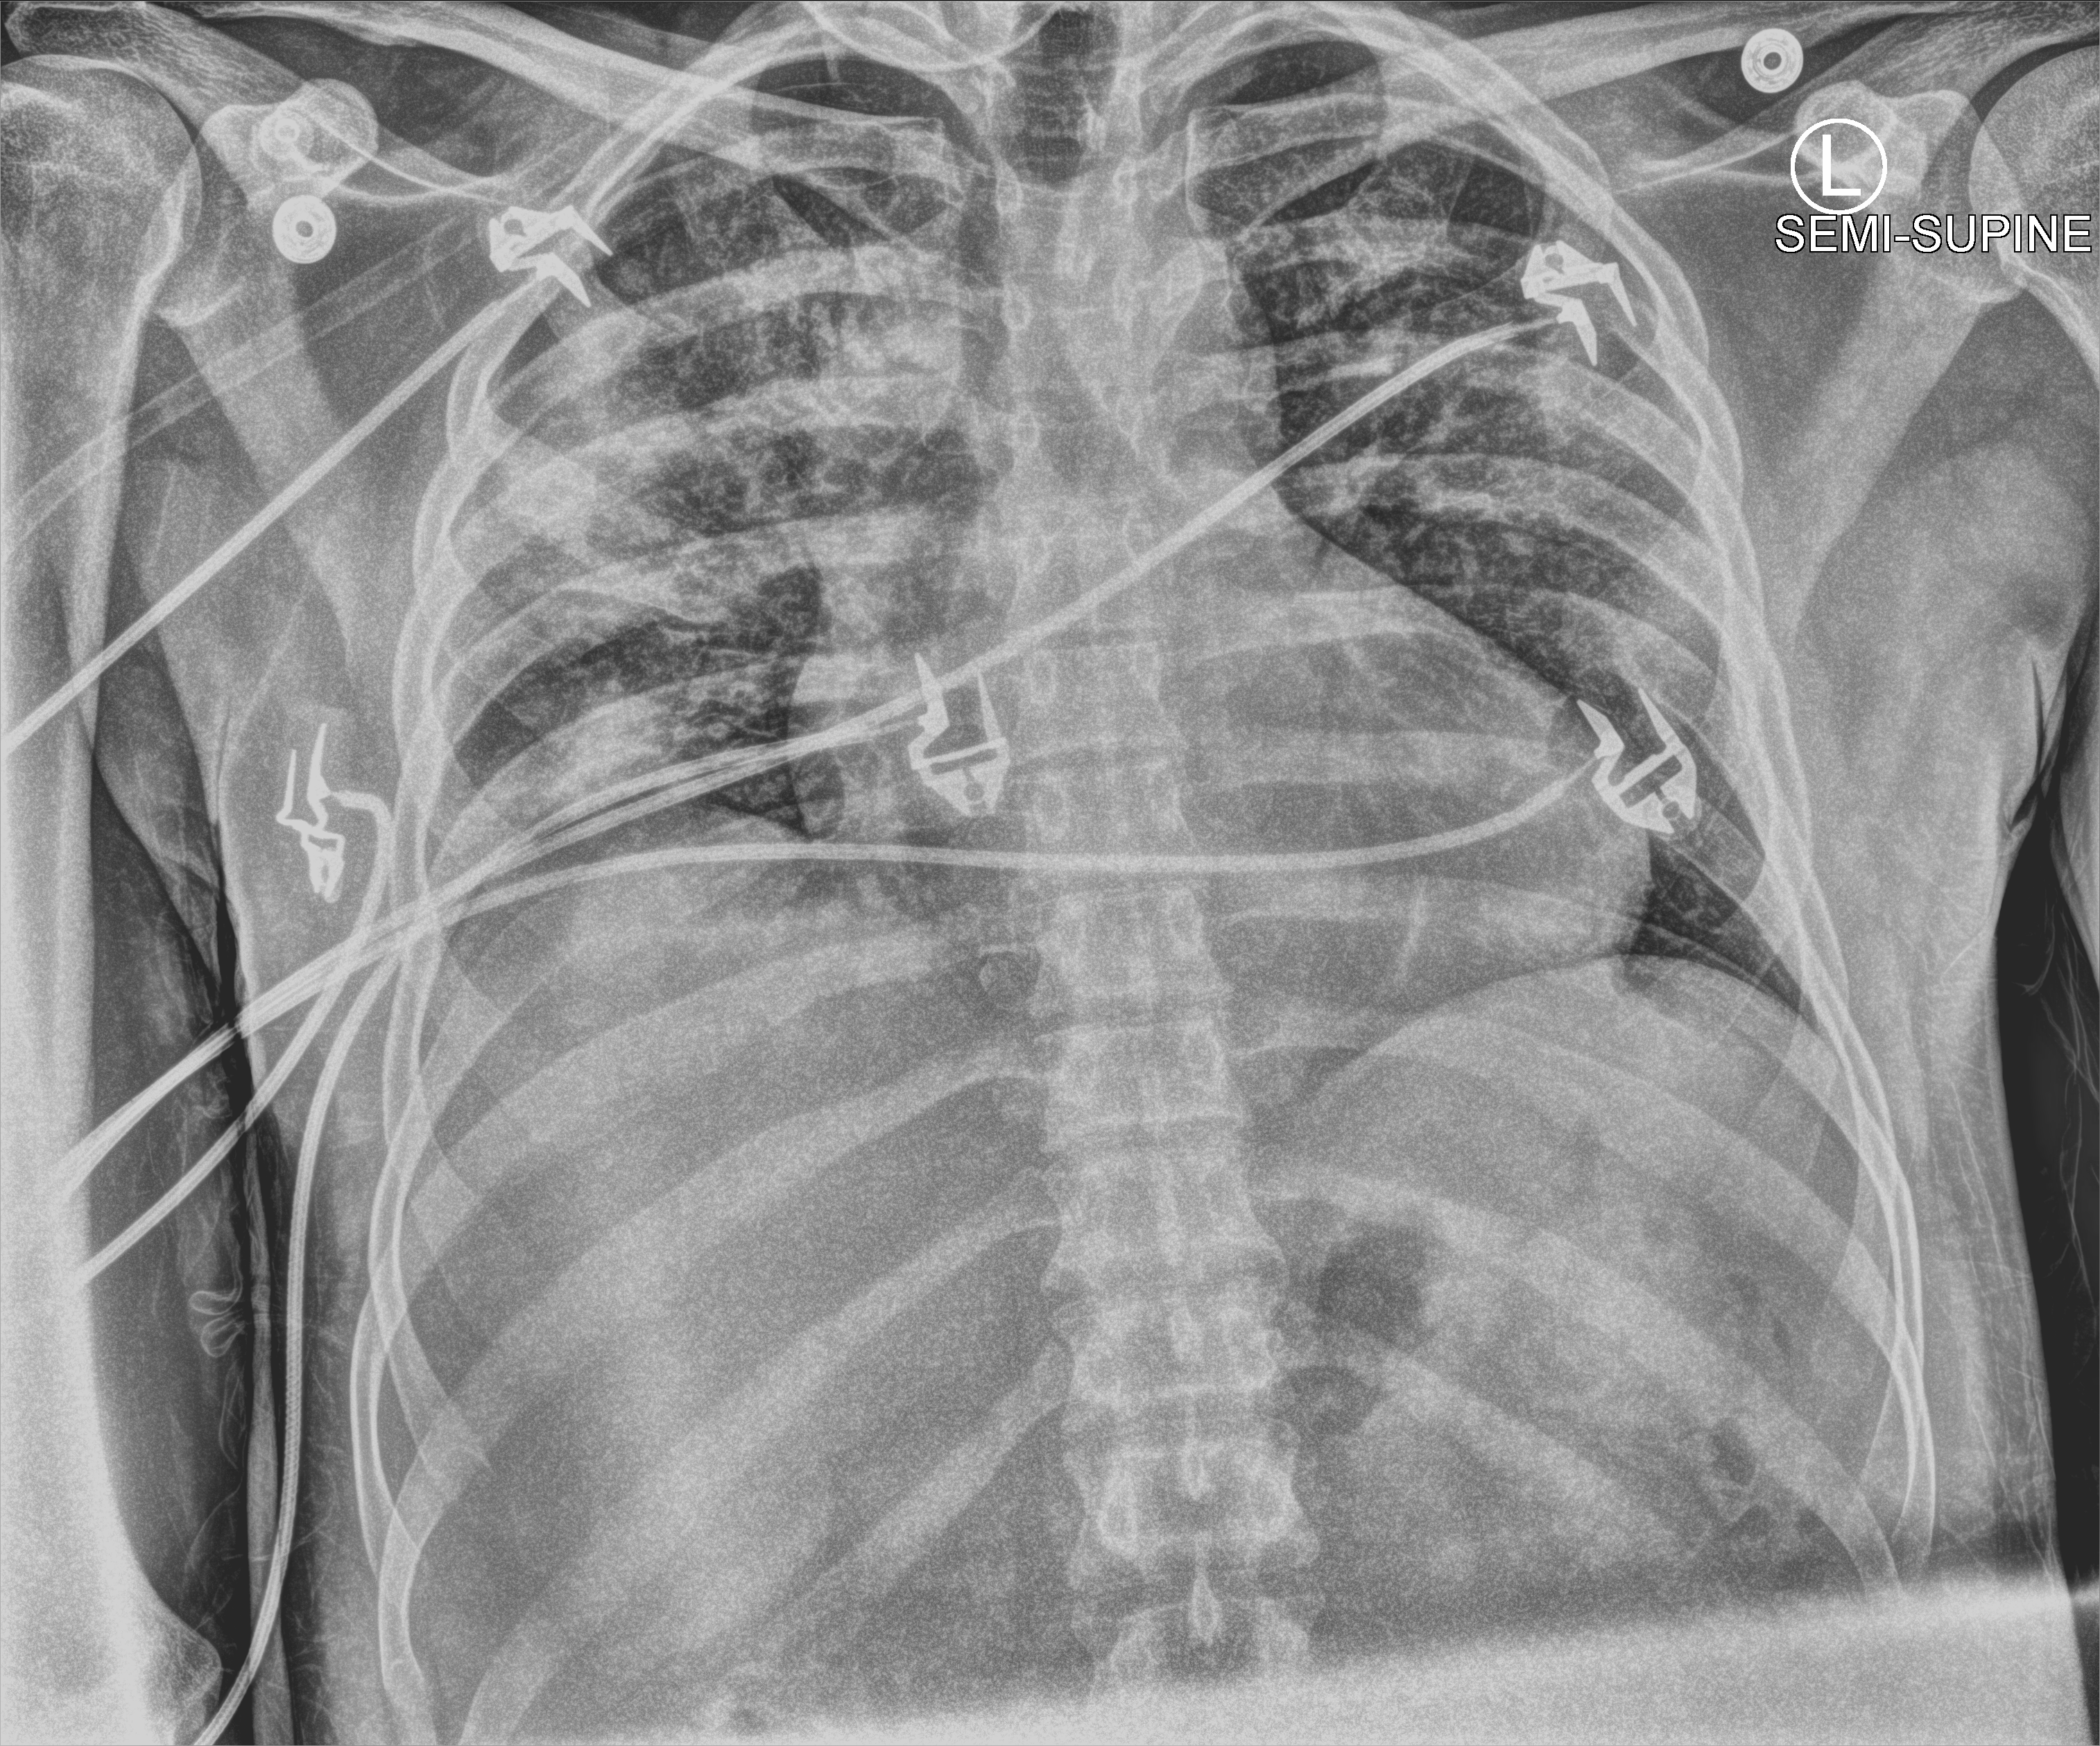
Chest X-ray (portable), anteroposterior (AP) projection. Patient hospitalised with COVID-19; male, aged 18–59 years.
Admission-level facts for this patient (not findings on this image; timing relative to this image not recorded): other chronic lung disease (admission record): no; admitted to intensive care during this hospital stay: no; mechanically ventilated during this hospital stay: no.